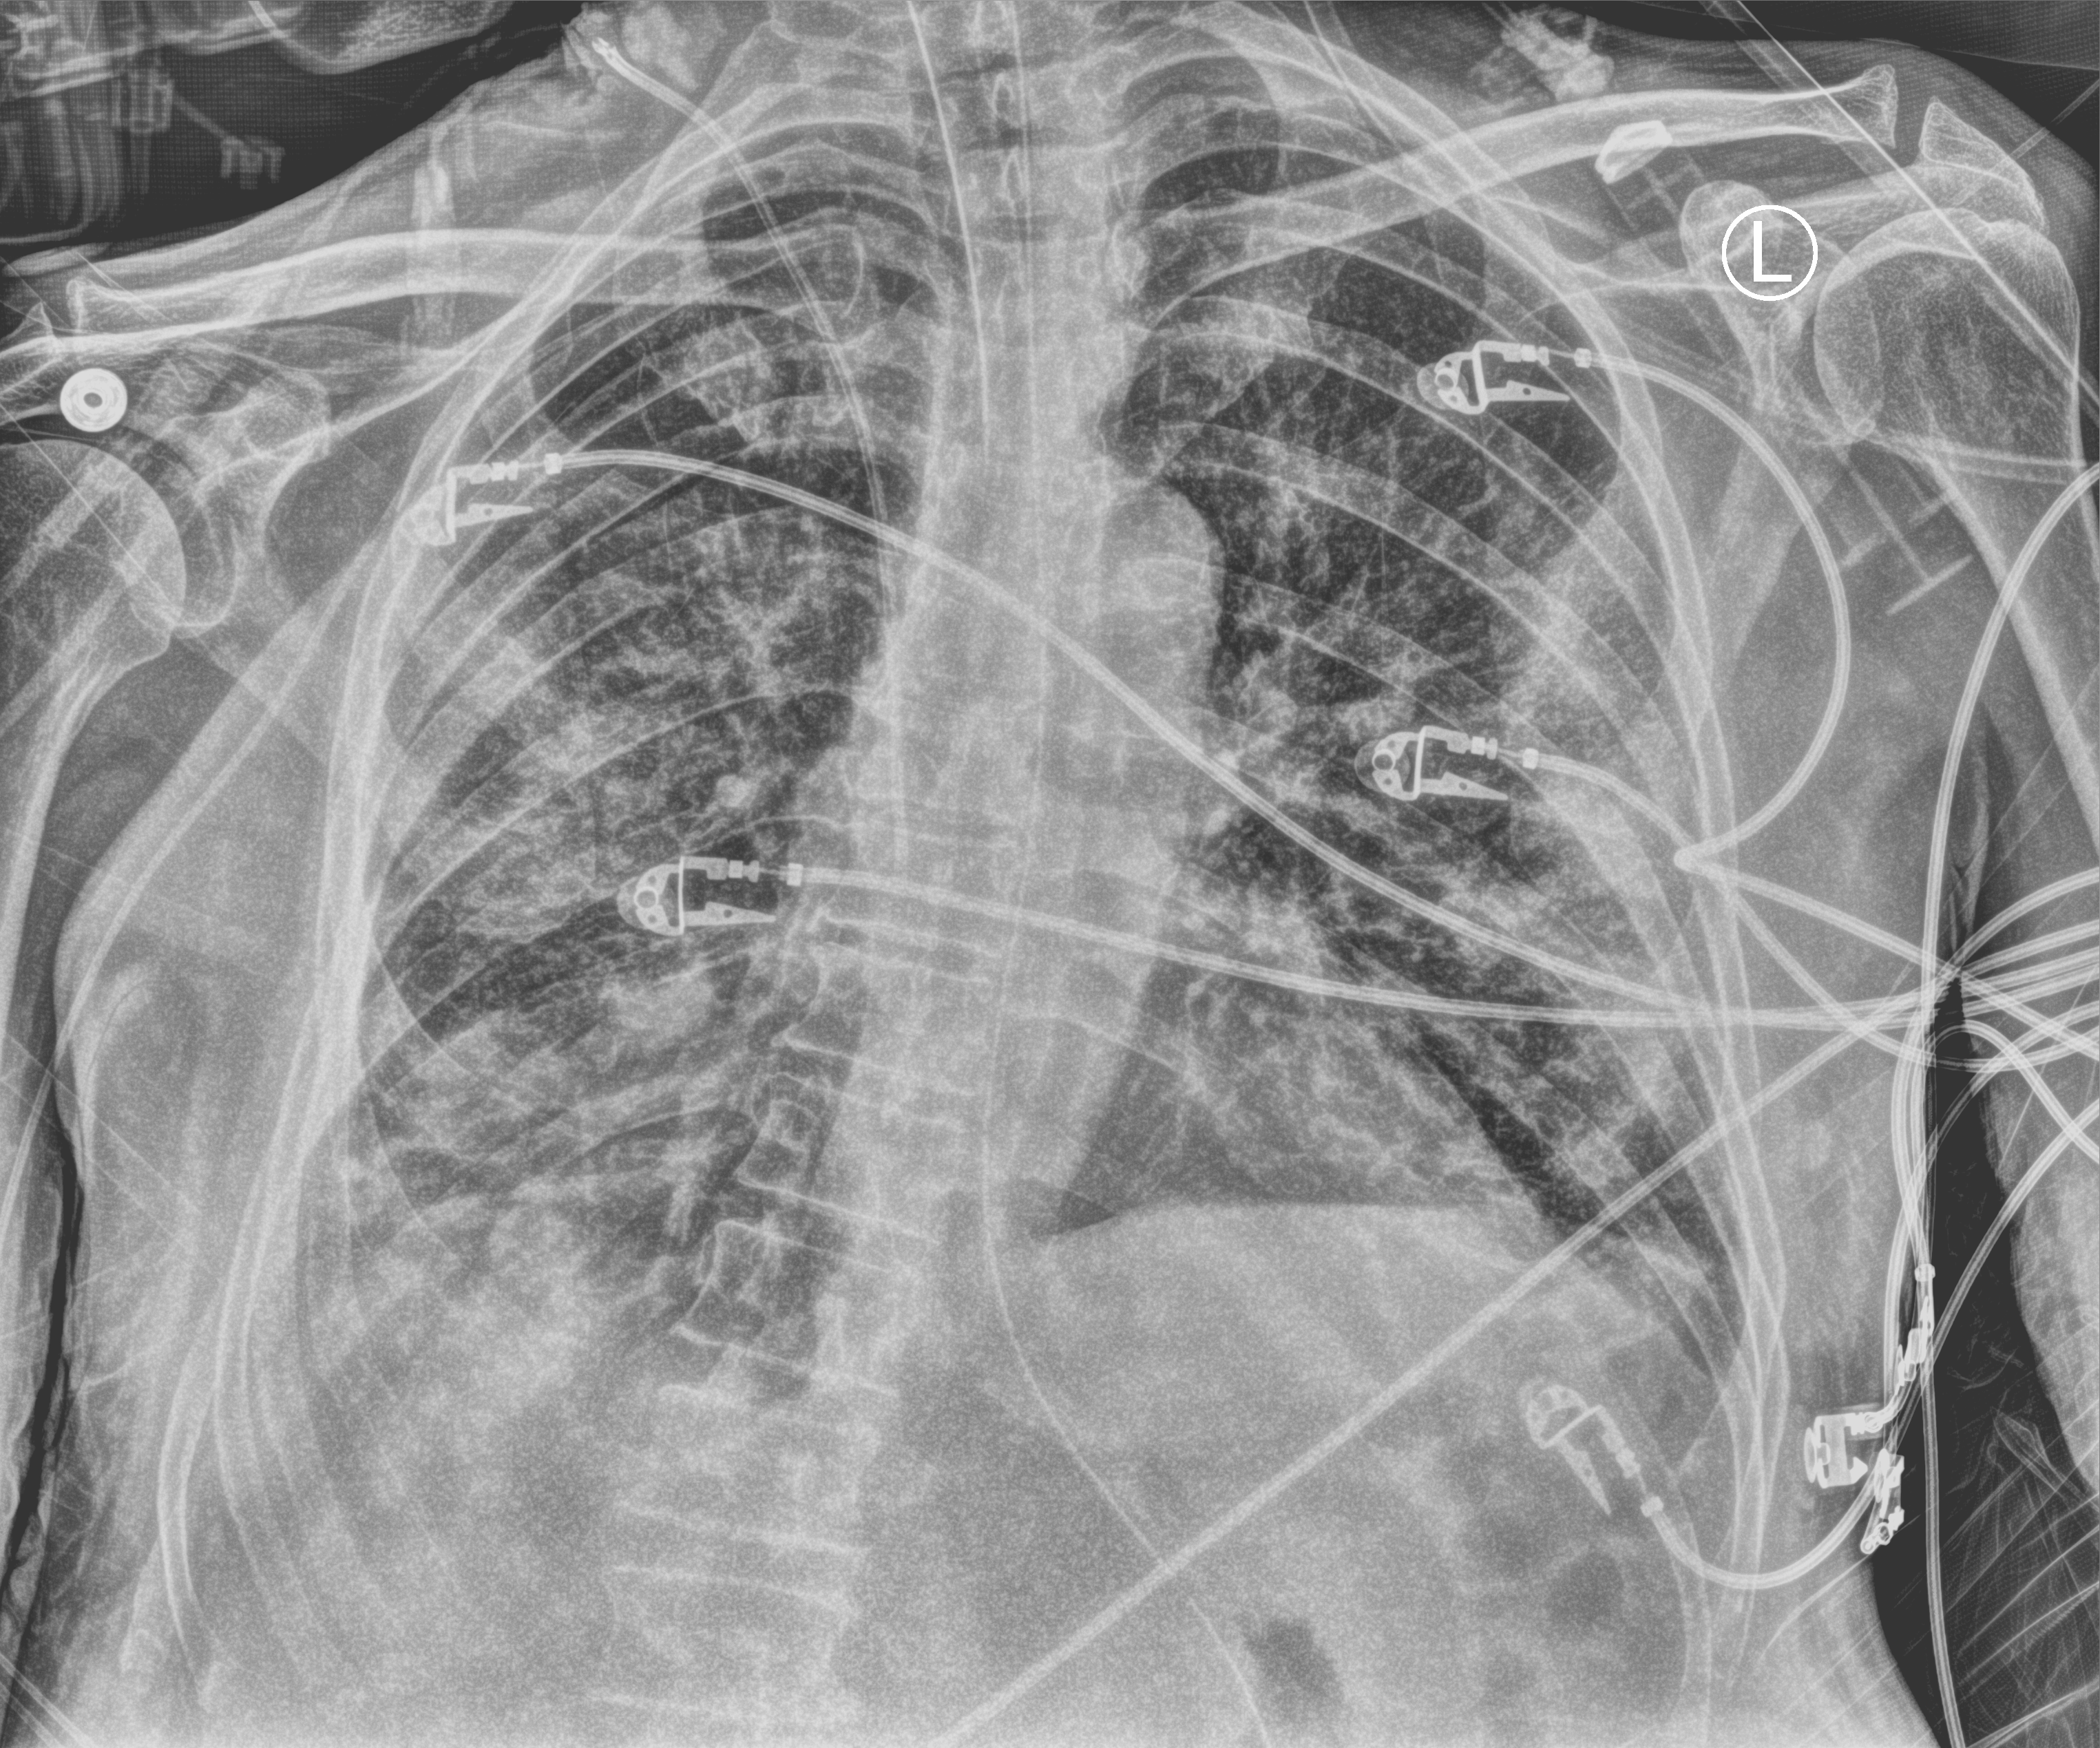
Portable chest radiograph; anteroposterior (AP) projection. Male patient hospitalised with COVID-19, age 75–90 years.
Hospital-stay facts (about this admission, not read from this image; timing relative to this image not recorded): mechanically ventilated during this hospital stay: yes; chronic kidney disease (admission record): no.